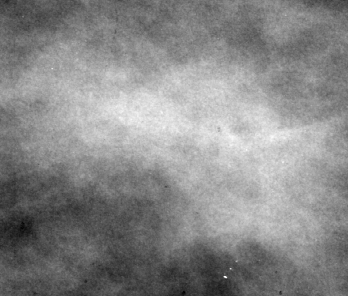
Crop from a digitized film mammogram around one marked abnormality, right breast, CC view, BI-RADS breast density category 3 (scale 1–4).
Finding: mass, shape architectural distortion, margins ill defined; BI-RADS assessment category 4; subtlety rating 2 on a 1 (subtle) to 5 (obvious) scale; pathology (as recorded): malignant.